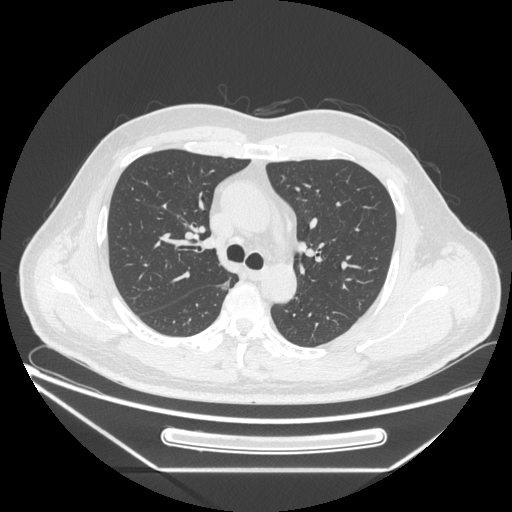
Chest CT, one axial slice. Position 169 of 271 along the scan axis. 120 kVp. Lung window (W 1500 / L -600 HU). 1.25 mm slice thickness. 512 × 512 image matrix, field of view 414 × 414 mm. Patient: male, 49 years. Case-level facts recorded for this patient, not image findings: clinical TNM (as recorded): T1b N0 M0; histopathological grade: G2.
Outlined on this slice (bounding box drawn by a radiologist):
- lung tumour (recorded histology: adenocarcinoma): bounding box <216,276,235,295> (left, top, right, bottom; pixels)